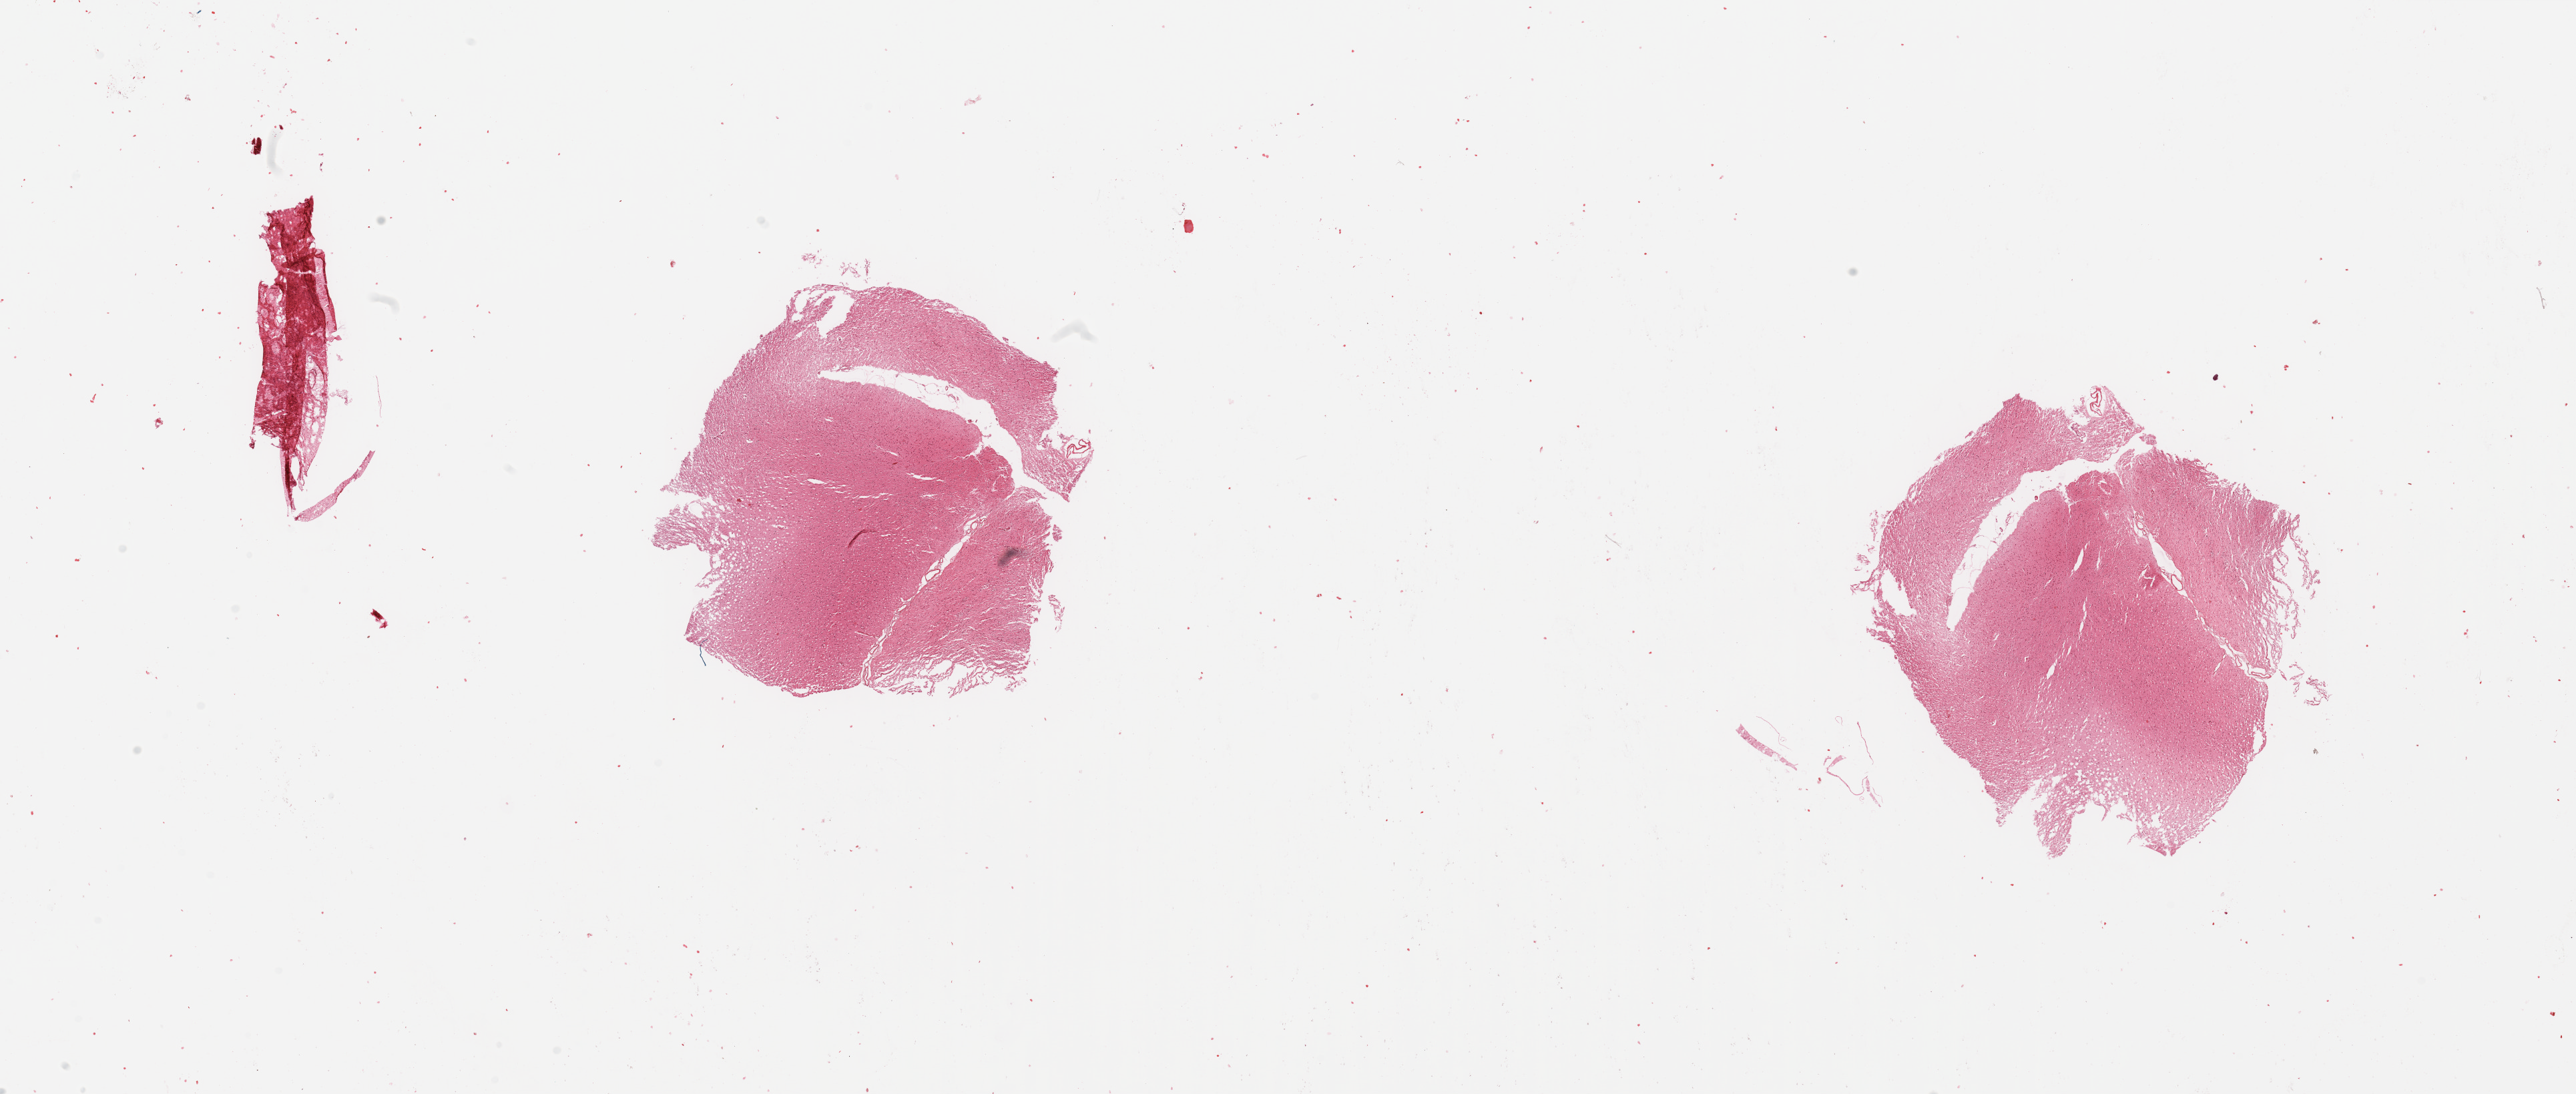
Whole-slide histology image, H&E-stained, shown as a low-resolution overview of the whole scanned area (about 30.5 x 13.0 mm, acquisition: 20x scan). Tumour tissue sample, sampled site: frontal lobe. Male, 77 y/o. Composition of this section per pathologist review: tumour nuclei 80%, necrosis 3%.
Primary tumour site (as recorded): frontal lobe. Histologic diagnosis: Glioblastoma.